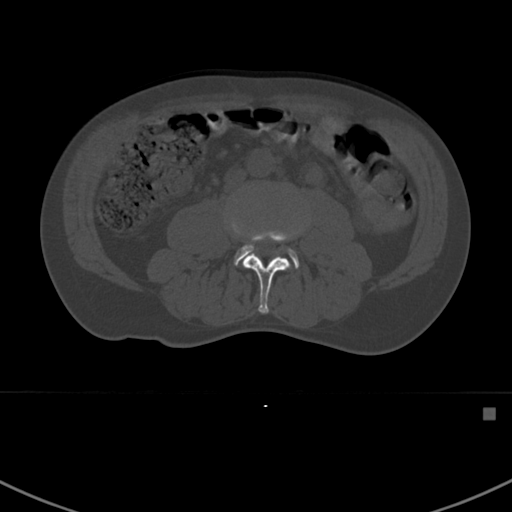
CT including the spine, one axial slice. Position 256 of 412 along the scan axis. Reconstruction kernel Br40s. 120 kVp. Bone window (W 1800 / L 400 HU). 1.5 mm slice thickness. 512 × 512 image matrix, field of view 358 × 358 mm. Patient: male, 59 years. Case-level facts recorded for this patient, not image findings: primary cancer: prostate.
Structures marked on this image (semi-automatically segmented with operator editing):
- L3 vertebra: bounding box (x1, y1, x2, y2) in pixels: (230, 211, 303, 314)
- L4 vertebra: (233, 244, 299, 269)